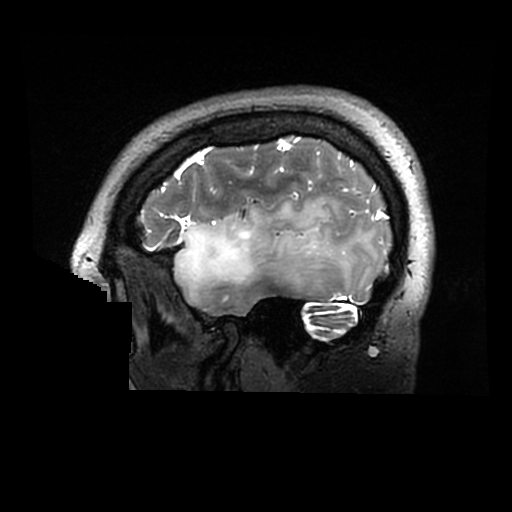
Brain MRI from a brain-tumour surgery series, one sagittal slice; position 236 of 320 along the scan axis; 0.6 mm slice thickness; 512 × 512 image matrix, field of view 240 × 240 mm. From the clinical record (not read from this slice): histopathology: Astrocytoma; WHO grade: 2; IDH mutation: yes.
Structures marked on this image (manually delineated by an expert):
- tumour: bounding box [x1, y1, x2, y2] px = [173, 197, 378, 298]